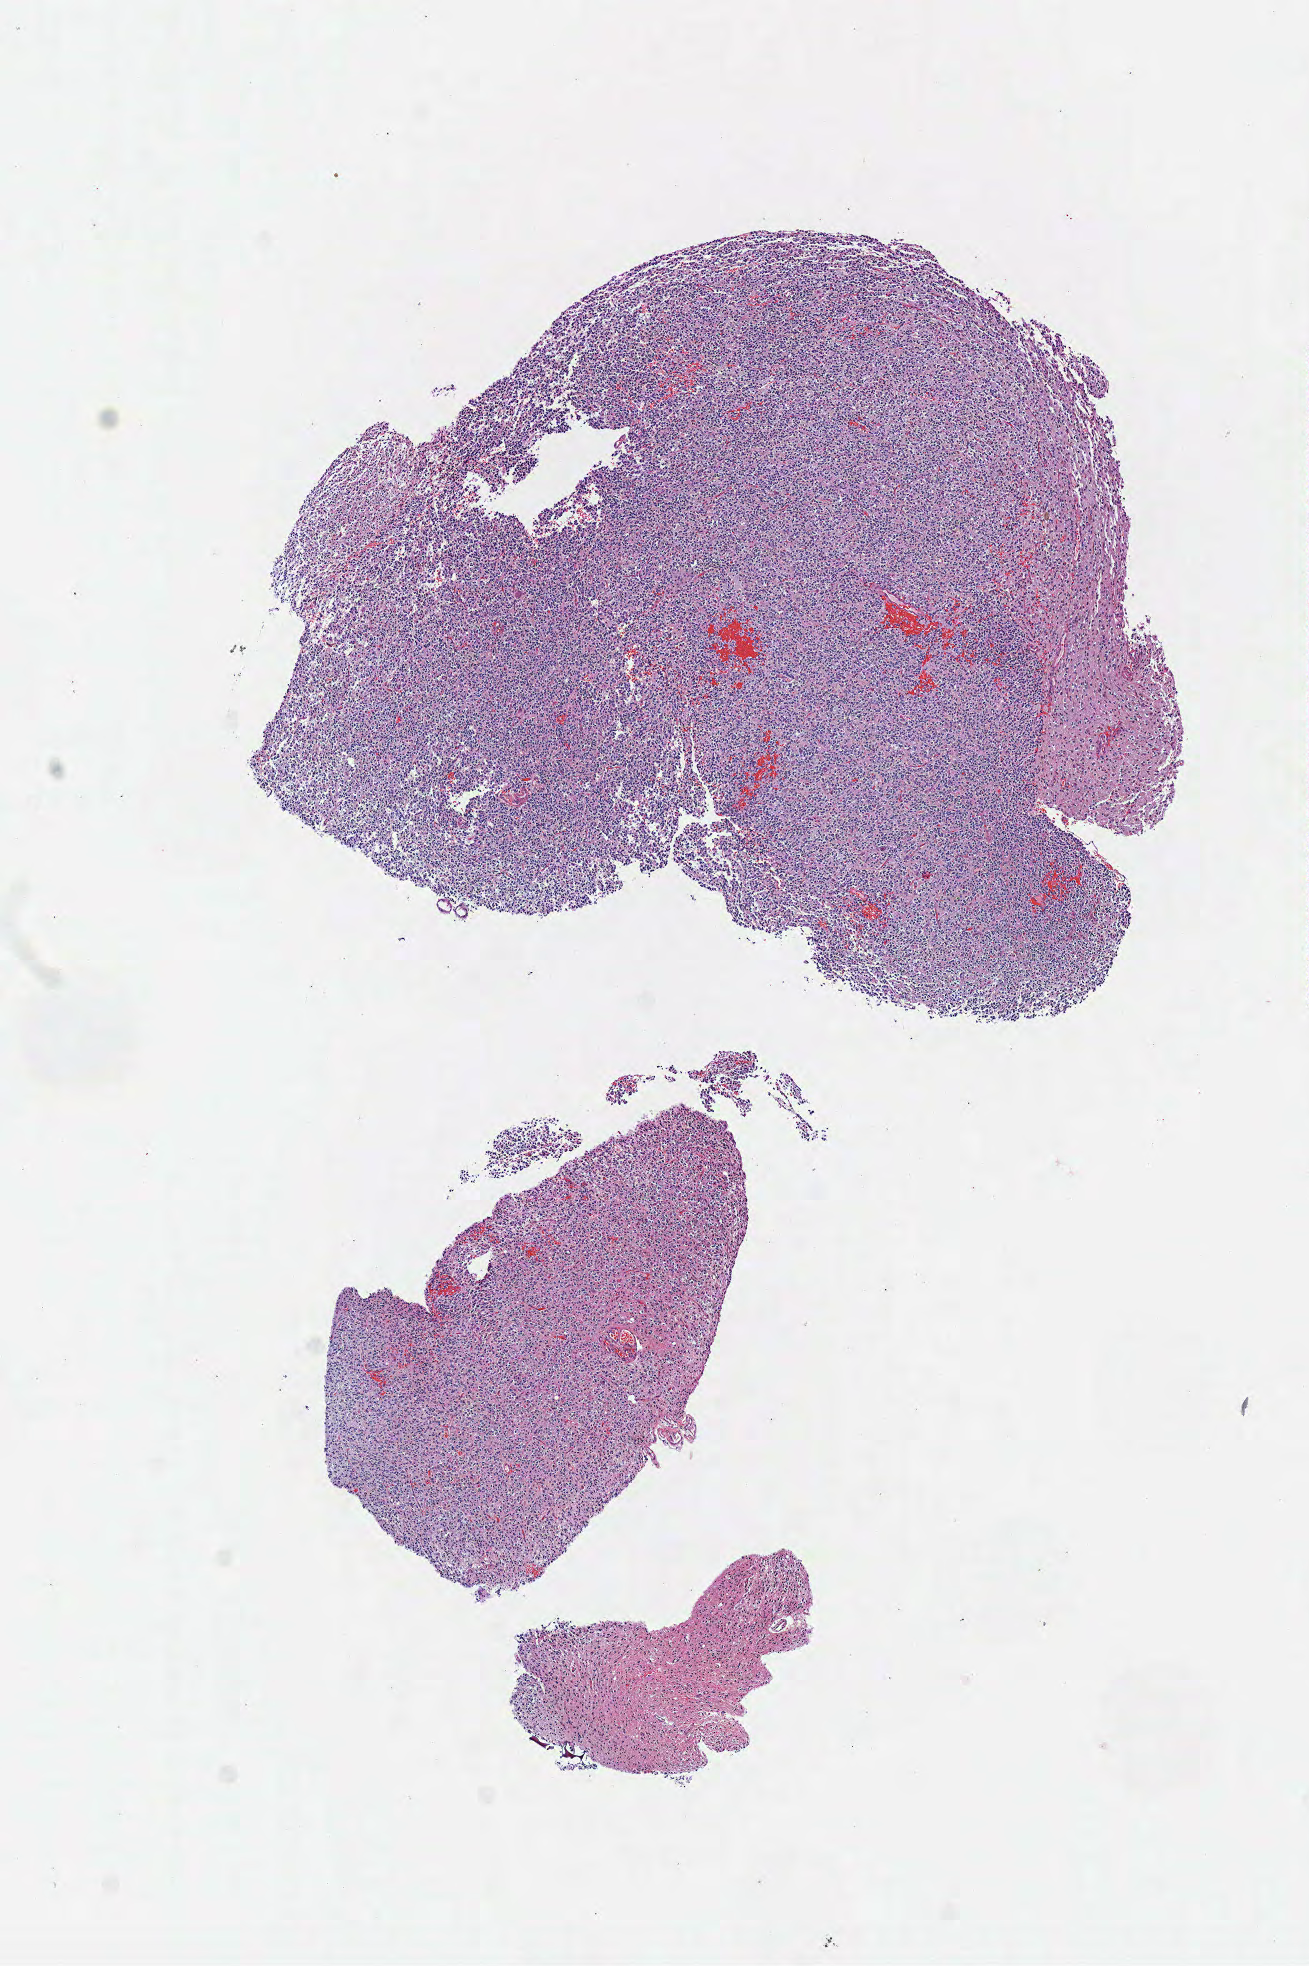
Whole-slide histology image, Hematoxylin and eosin (H&E) stained — shown as a low-resolution overview of the whole scanned area (about 5.2 x 7.7 mm); frozen section from the top of the tissue portion; brain, primary tumour sample. Female, age 62 years at initial diagnosis.
Diagnosis: Oligodendroglioma, NOS.